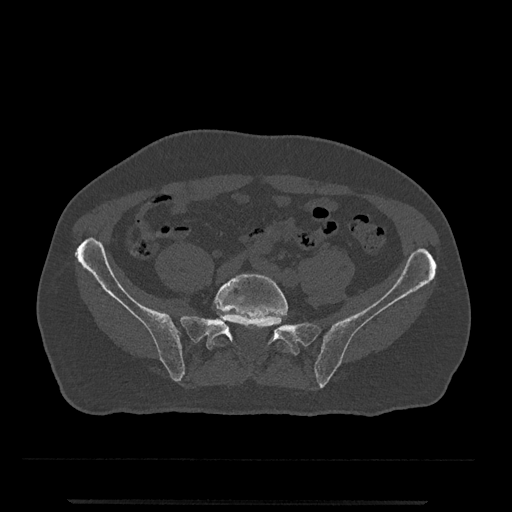
CT including the spine, one axial slice; reconstruction kernel Br40s/3; bone window (W 1800 / L 400 HU); 0.5 mm slice thickness; 512 × 512 image matrix. Male patient, age 63 years. Case-level facts recorded for this patient, not image findings: primary cancer: prostate.
Outlined on this slice (semi-automatic segmentation, software-assisted and operator-edited):
- L5 vertebra: box from (x=209, y=274) to (x=289, y=352) px